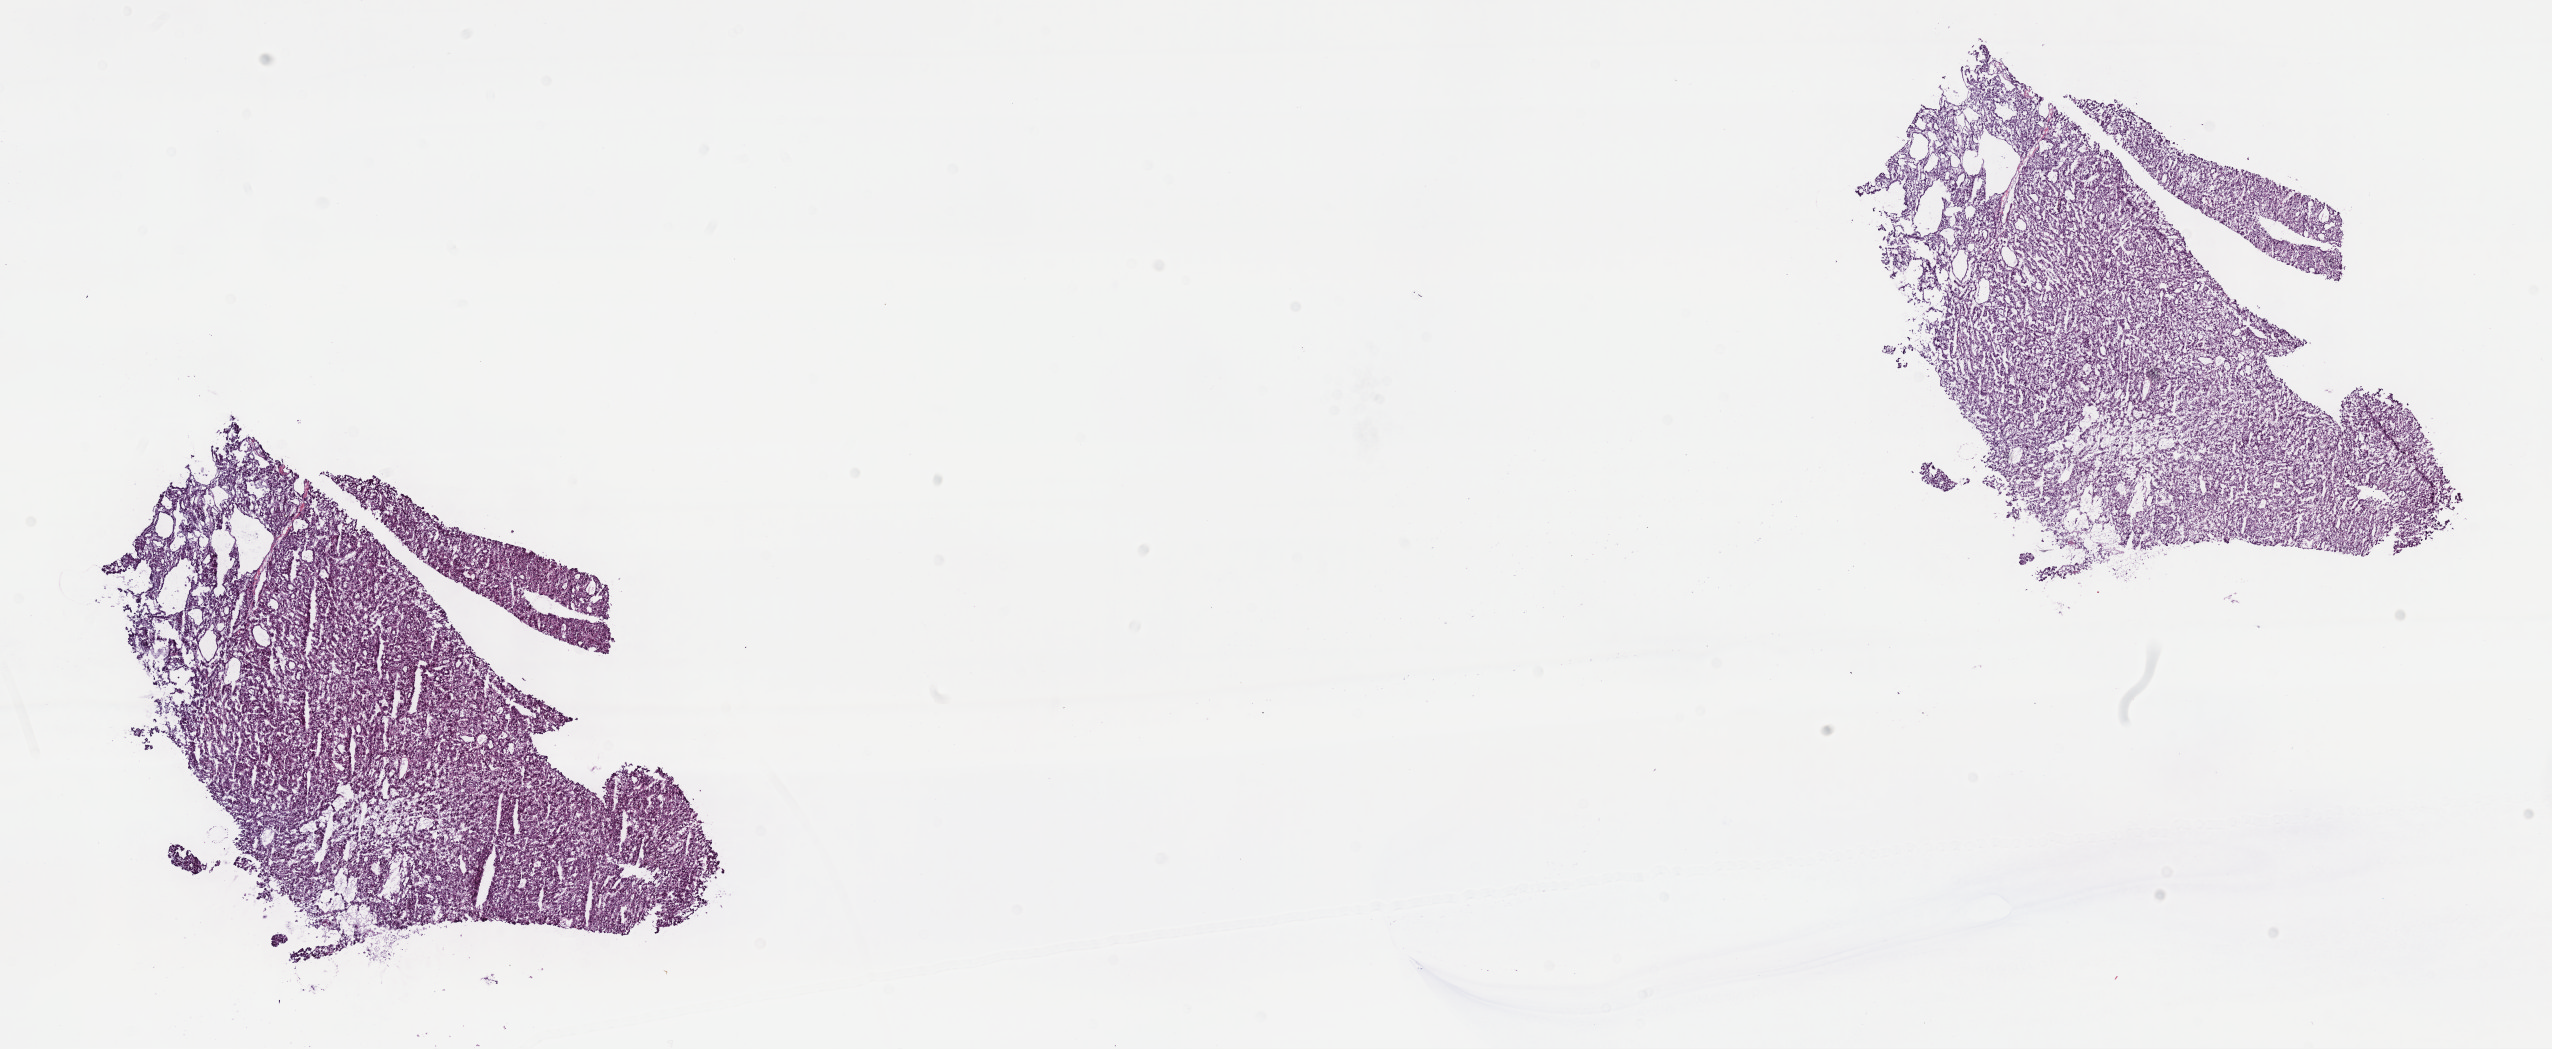
Digitized H&E tissue section (whole slide) — shown as a low-resolution overview of the whole scanned area (about 20.6 x 8.5 mm). Frozen section from the top of the tissue portion. Sample: primary tumour, liver. Patient: male, age at initial diagnosis 55 years. Histologic grade: G2 (moderately differentiated). Composition of this section per pathologist review: tumour cells 85%, tumour nuclei 85%, normal cells 0%, stromal cells 15%, necrosis 0%. Infiltration values recorded for this section: lymphocyte infiltration 3%, monocyte infiltration 1%, neutrophil infiltration 1%.
AJCC pathologic stage: II (7th edition). Pathologic diagnosis: Hepatocellular carcinoma, NOS.